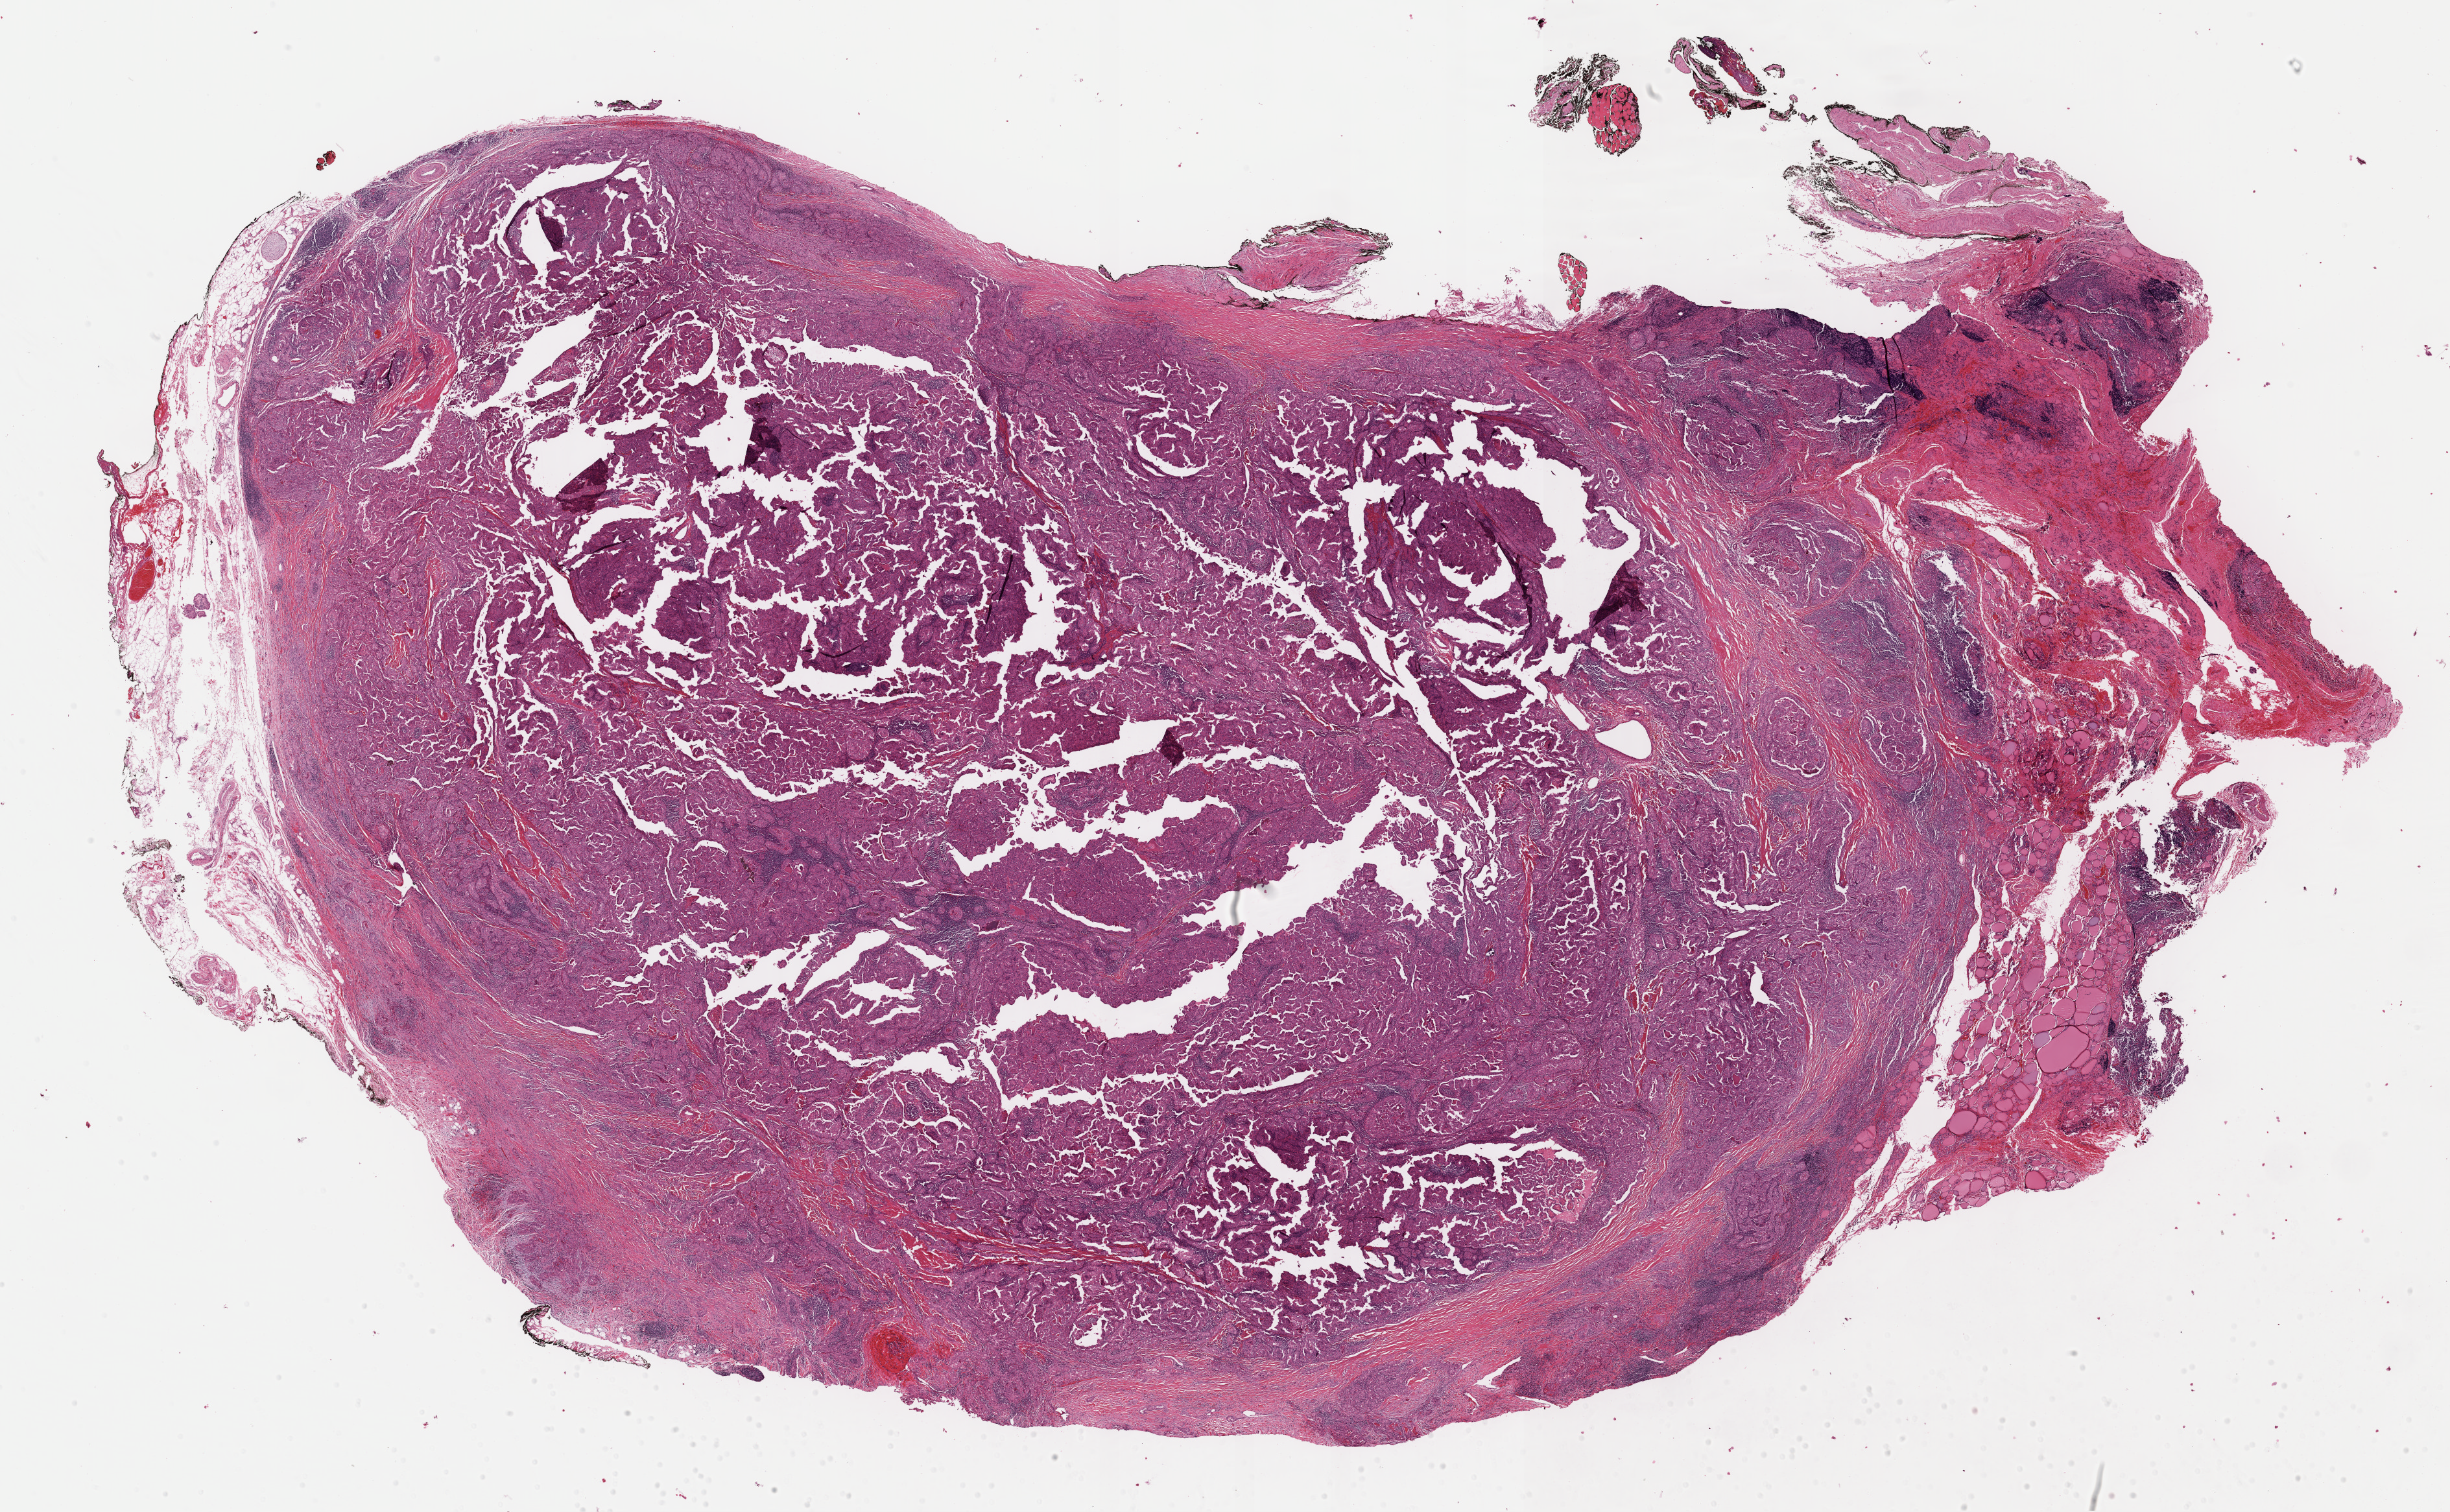
H&E-stained whole-slide image — whole scanned area (about 29.8 x 18.4 mm, slide scanned at 40x) shown as a low-resolution overview. Formalin-fixed paraffin-embedded (FFPE) diagnostic section. Primary tumour sample from the thyroid. Female, age 69 years at initial diagnosis.
Laterality: right. AJCC pathologic stage: I (7th edition). Diagnosis: Papillary adenocarcinoma, NOS (thyroid gland). TNM: T1a N0 M0. Lymph nodes positive (case pathology): 0 of 6 examined.